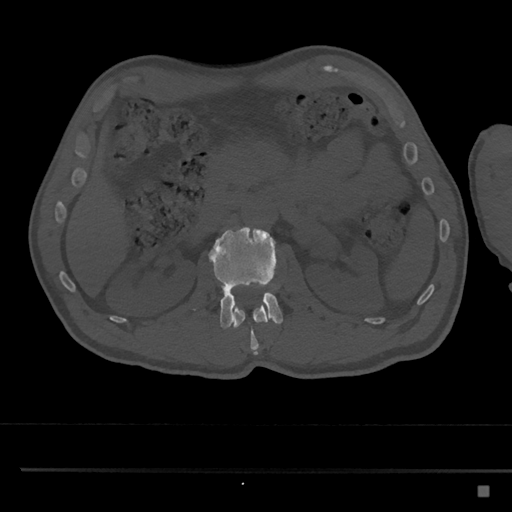
CT including the spine, one axial slice; slice 788 of 797 in the series (ordered by position); reconstruction kernel Br40s/3; bone window (W 1800 / L 400 HU); 512 × 512 image matrix, field of view 391 × 391 mm. Male patient, age 59 years. From the clinical record (not read from this slice): primary cancer: prostate.
Structures marked on this image (semi-automatic segmentation, software-assisted and operator-edited):
- L1 vertebra: box from (x=233, y=300) to (x=269, y=355) px
- L2 vertebra: (x=192, y=226)–(x=283, y=329)